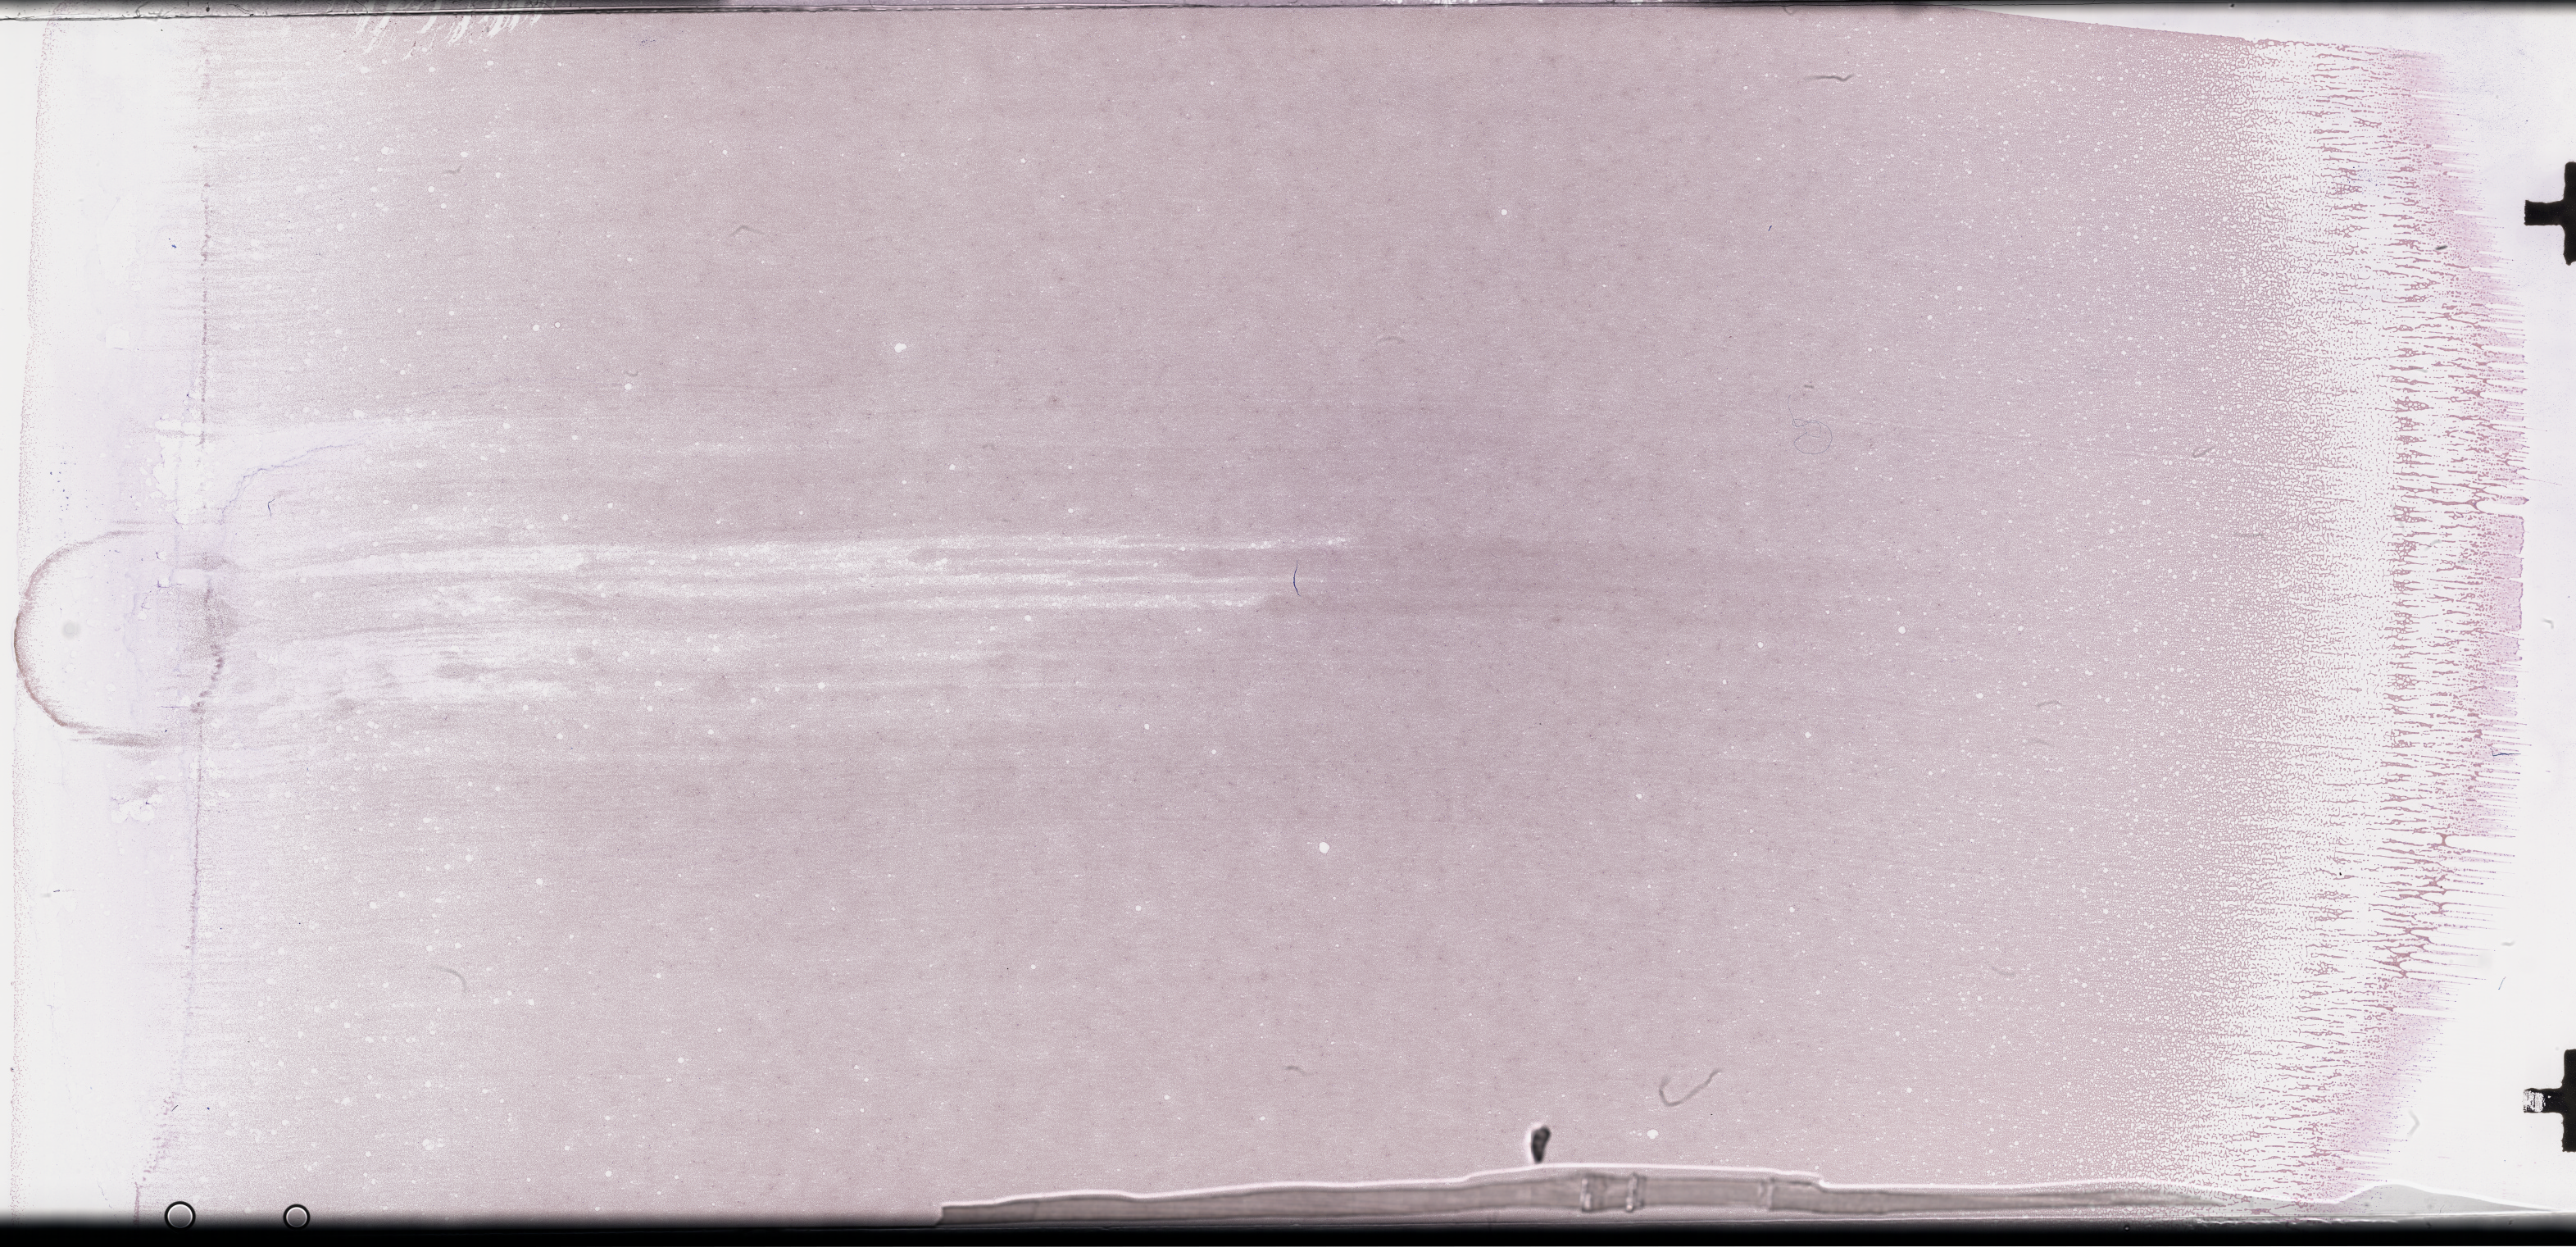
Whole-slide image of a whole blood smear, Wright–Giemsa stain — low-resolution overview of the scanned area, about 50.8 x 24.6 mm; smear from an EDTA sample; collected on treatment. Patient: male.
From a patient with: Plasma Cell Myeloma.